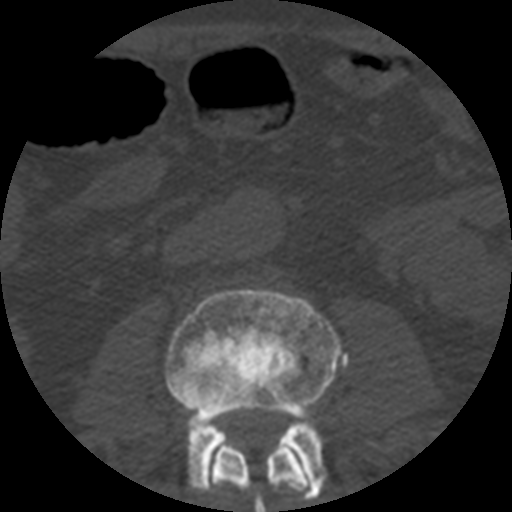
CT including the spine, one axial slice; slice 132 of 508 in the series (ordered by position); bone window (W 1800 / L 400 HU); 1.25 mm slice thickness; 512 × 512 image matrix, field of view 160 × 160 mm. Patient age 57 years. From the clinical record (not read from this slice): primary cancer: prostate.
Annotated regions visible in this slice (semi-automatic segmentation, software-assisted and operator-edited):
- L2 vertebra: box from (x=203, y=432) to (x=313, y=512) px
- L3 vertebra: (x=165, y=289)–(x=348, y=501)